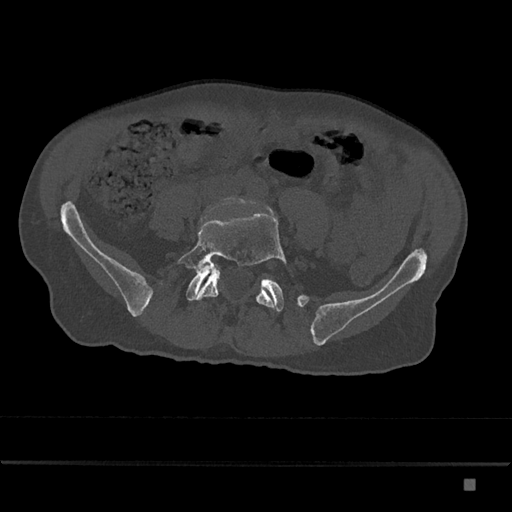
CT including the spine, one axial slice. Position 271 of 797 along the scan axis. Reconstruction kernel Br40s/3. 120 kVp. Bone window (W 1800 / L 400 HU). 512 × 512 image matrix. Male patient, age 72 years. From the clinical record (not read from this slice): primary cancer: prostate.
Outlined on this slice (semi-automatic segmentation, software-assisted and operator-edited):
- L5 vertebra: bounding box <178,212,286,308> (left, top, right, bottom; pixels)